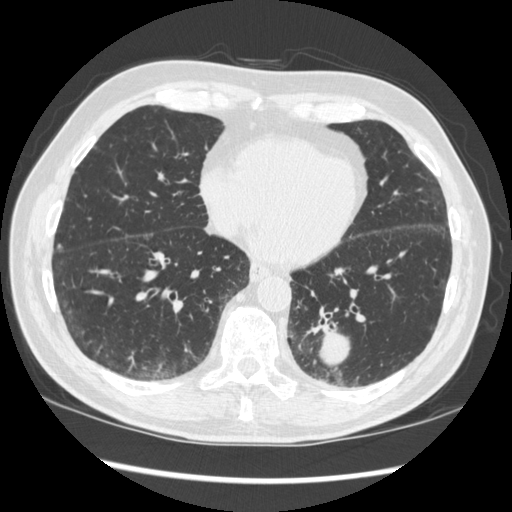
Axial slice from a low-dose chest CT screening exam. Baseline annual screen. Lung window (W 1500 / L -600 HU). 1.25 mm slice thickness. Standard (soft-tissue) reconstruction kernel (STANDARD). 512 × 512 image matrix, field of view 360 × 360 mm. Male participant, aged 72 years at enrolment.
Expert-annotated lung lesion, bounding box (x1, y1, x2, y2) in pixels: (274, 295, 378, 383). The screening reader recorded 2 non-calcified nodules or masses ≥4 mm on this exam (left lower lobe, right middle lobe); which of them this box marks is not recorded. Official screen result: positive, change unspecified: nodule(s) >= 4 mm or enlarging nodule(s), mass(es), or other non-specific abnormalities suspicious for lung cancer. Lung cancer was diagnosed 37 days after this screen: squamous cell carcinoma, NOS, left lower lobe, stage IIIA (AJCC 6th edition), 60 mm at pathology.